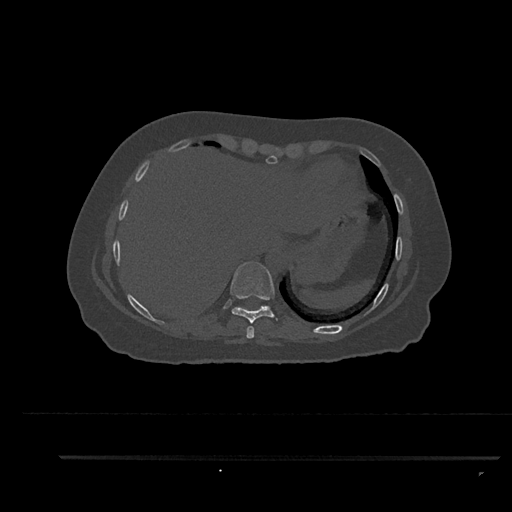
CT including the spine, one axial slice. Position 409 of 797 along the scan axis. 120 kVp. Bone window (W 1800 / L 400 HU). 0.5 mm slice thickness. 512 × 512 image matrix. Patient: female, 44 years. Case-level facts recorded for this patient, not image findings: primary cancer: renal; vertebrae with lytic lesions (as recorded): L1.
Outlined on this slice (semi-automatically segmented with operator editing):
- T8 vertebra: bounding box <246,326,255,339> (left, top, right, bottom; pixels)
- T9 vertebra: <230,262,278,324>